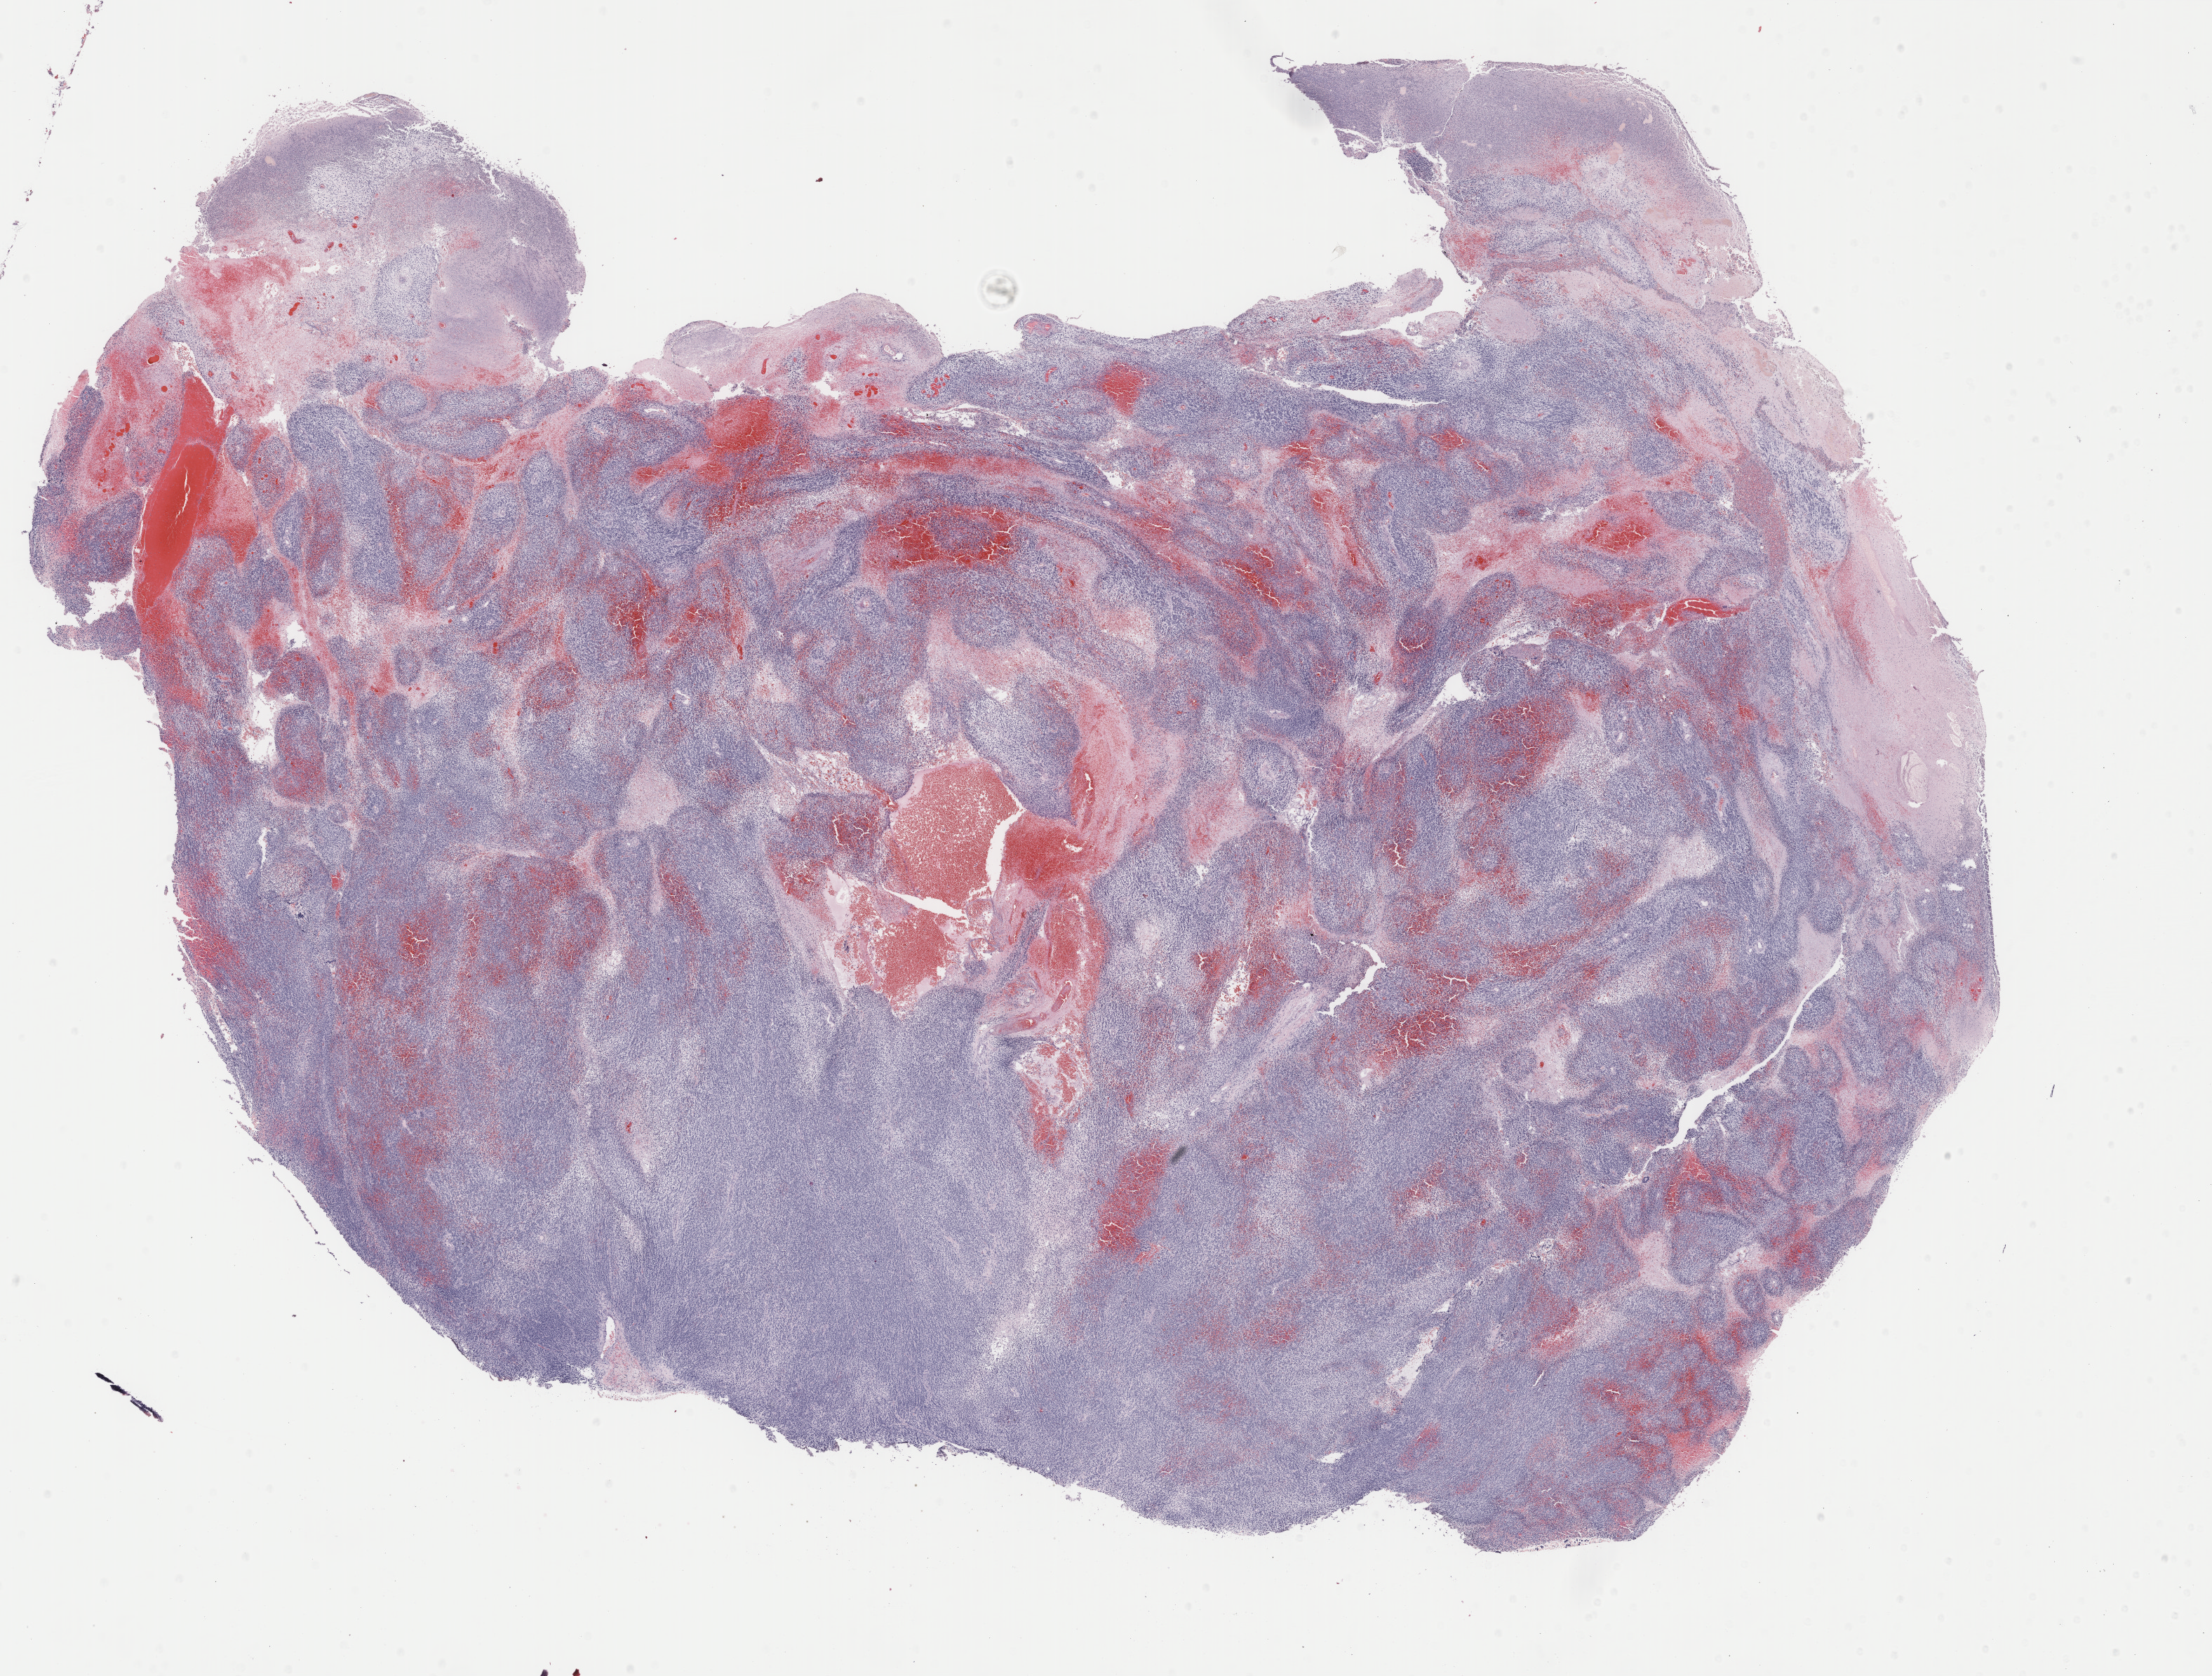
Whole-slide histology image, H&E — whole scanned area (about 25.0 x 19.0 mm, acquisition: 40x scan) shown as a low-resolution overview, FFPE section, sample: primary tumour, uterus. Female, age 67 years at initial diagnosis.
* FIGO stage: IIIC2
* pathologic diagnosis: Mullerian mixed tumor